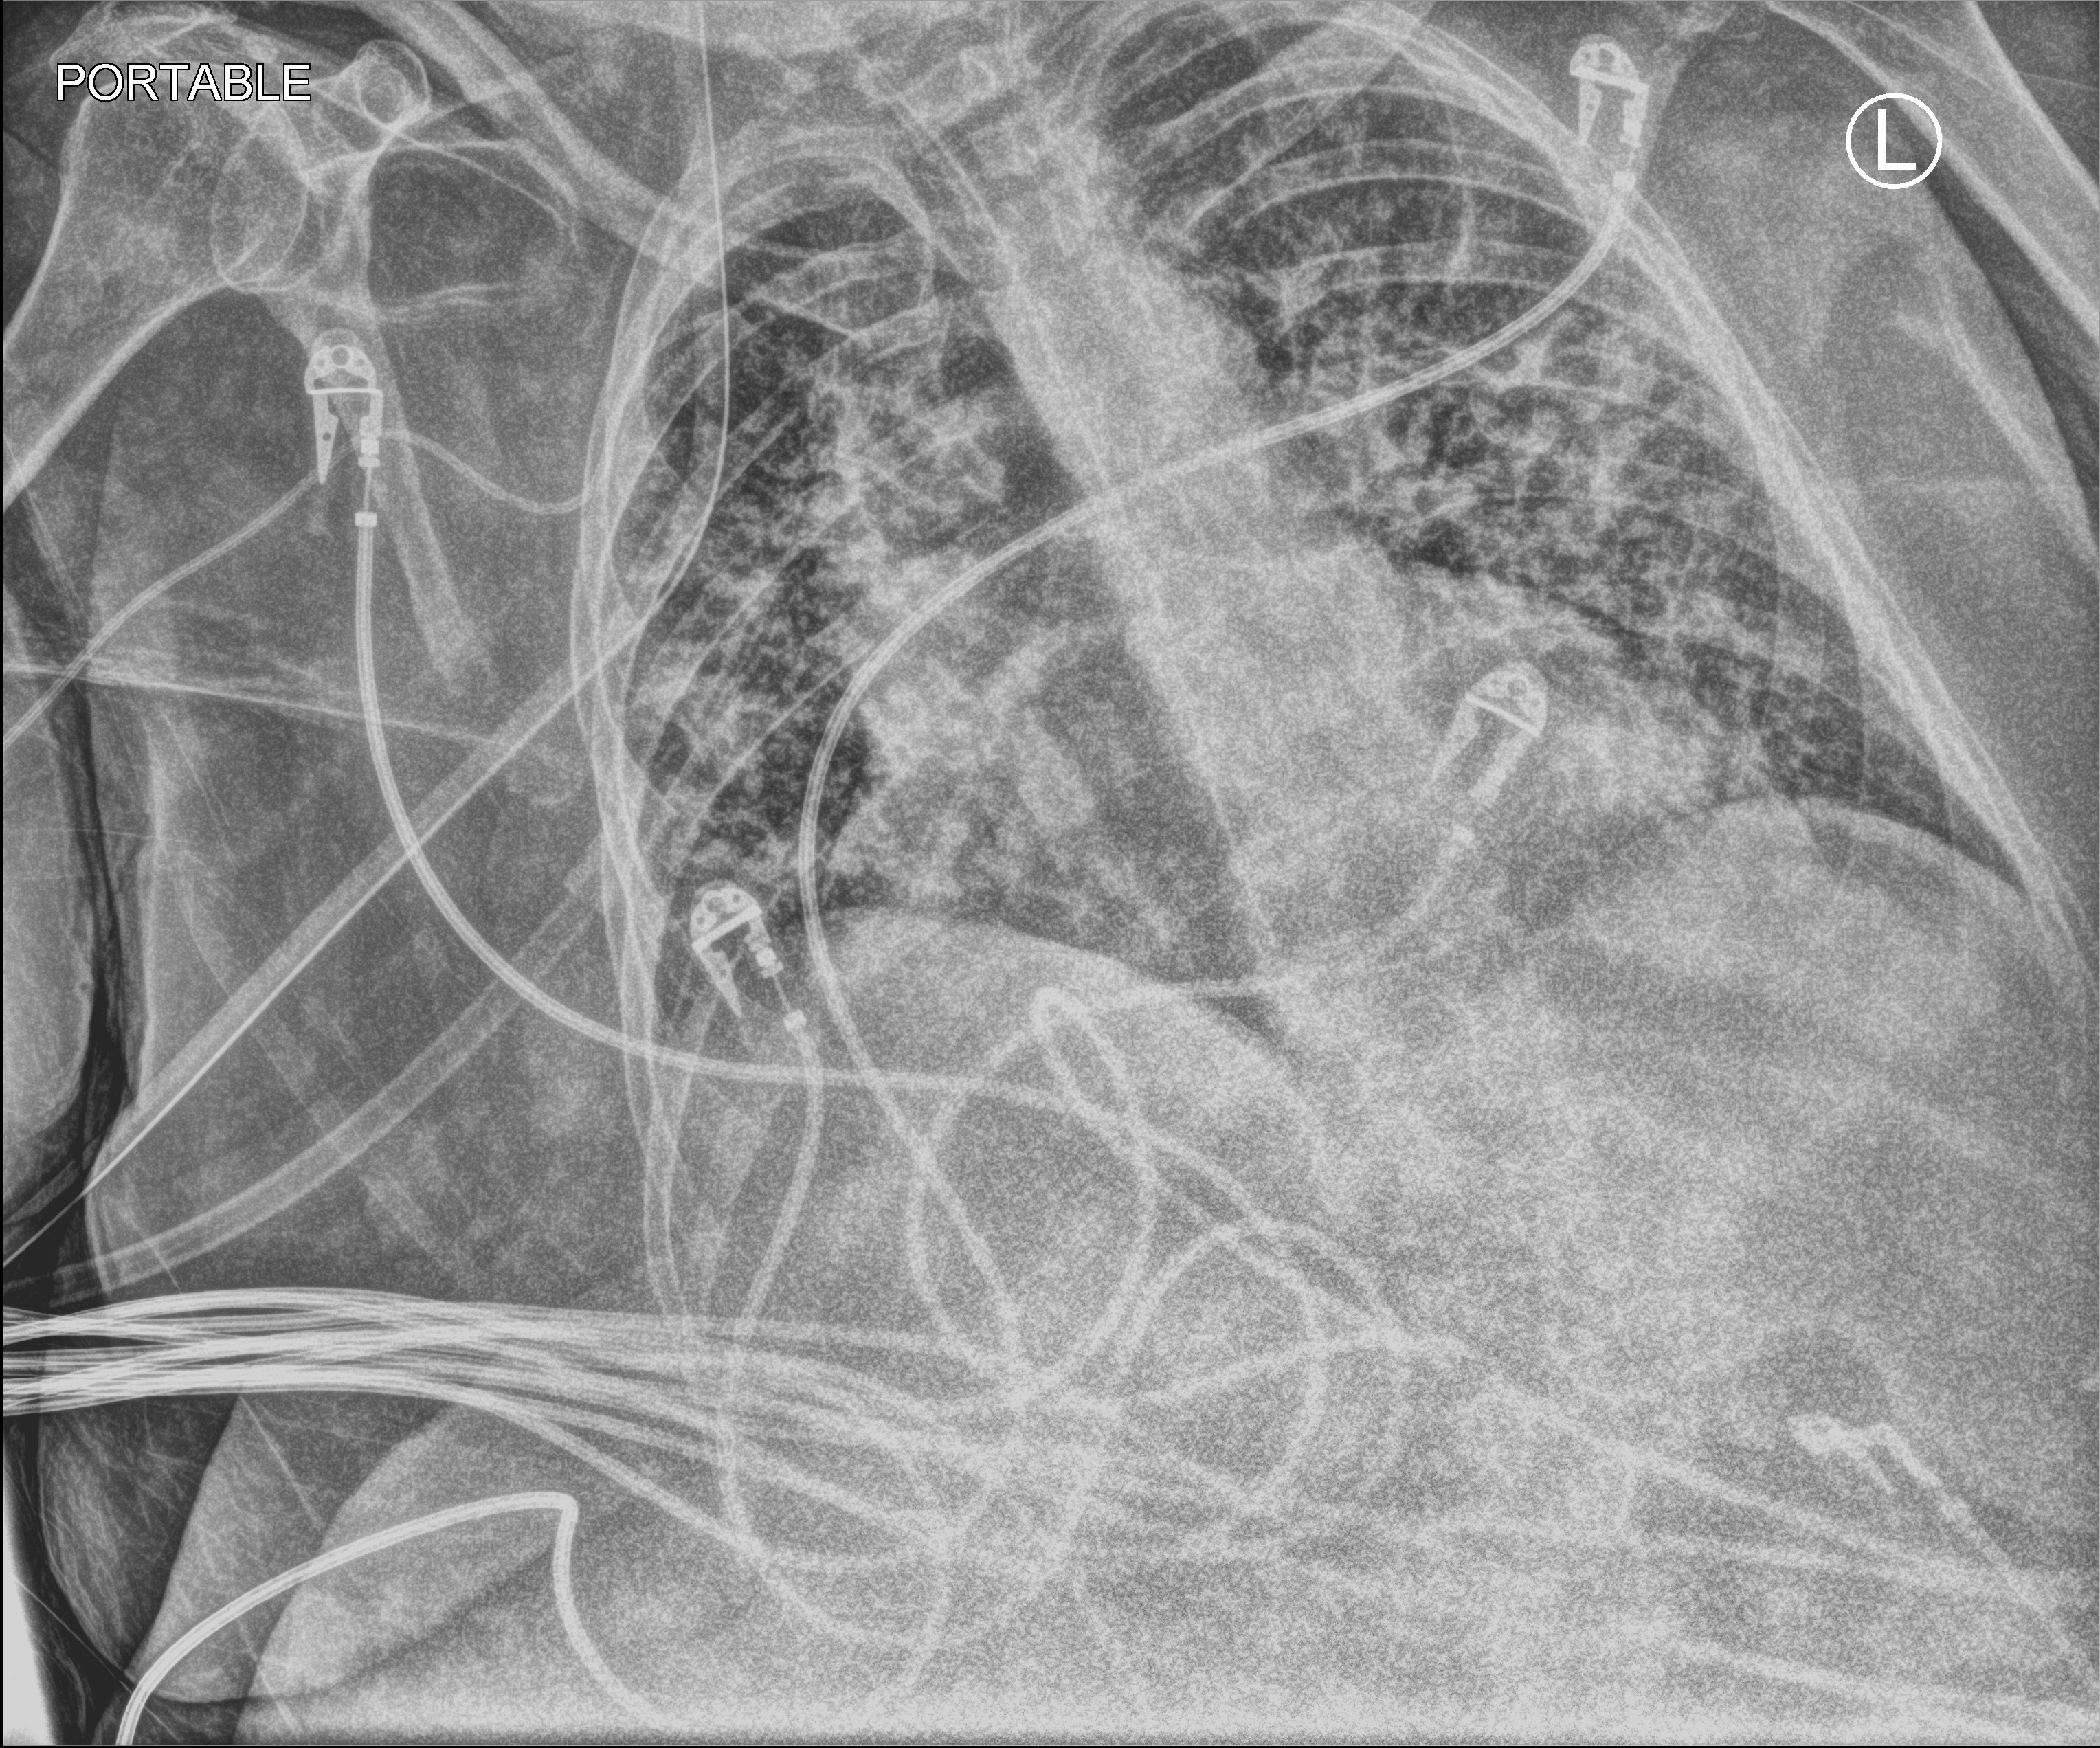
Portable chest radiograph. Female patient hospitalised with COVID-19, age 75–90 years.
Hospital-stay facts (about this admission, not read from this image; timing relative to this image not recorded): length of hospital stay: 31 days; mechanically ventilated during this hospital stay: yes.